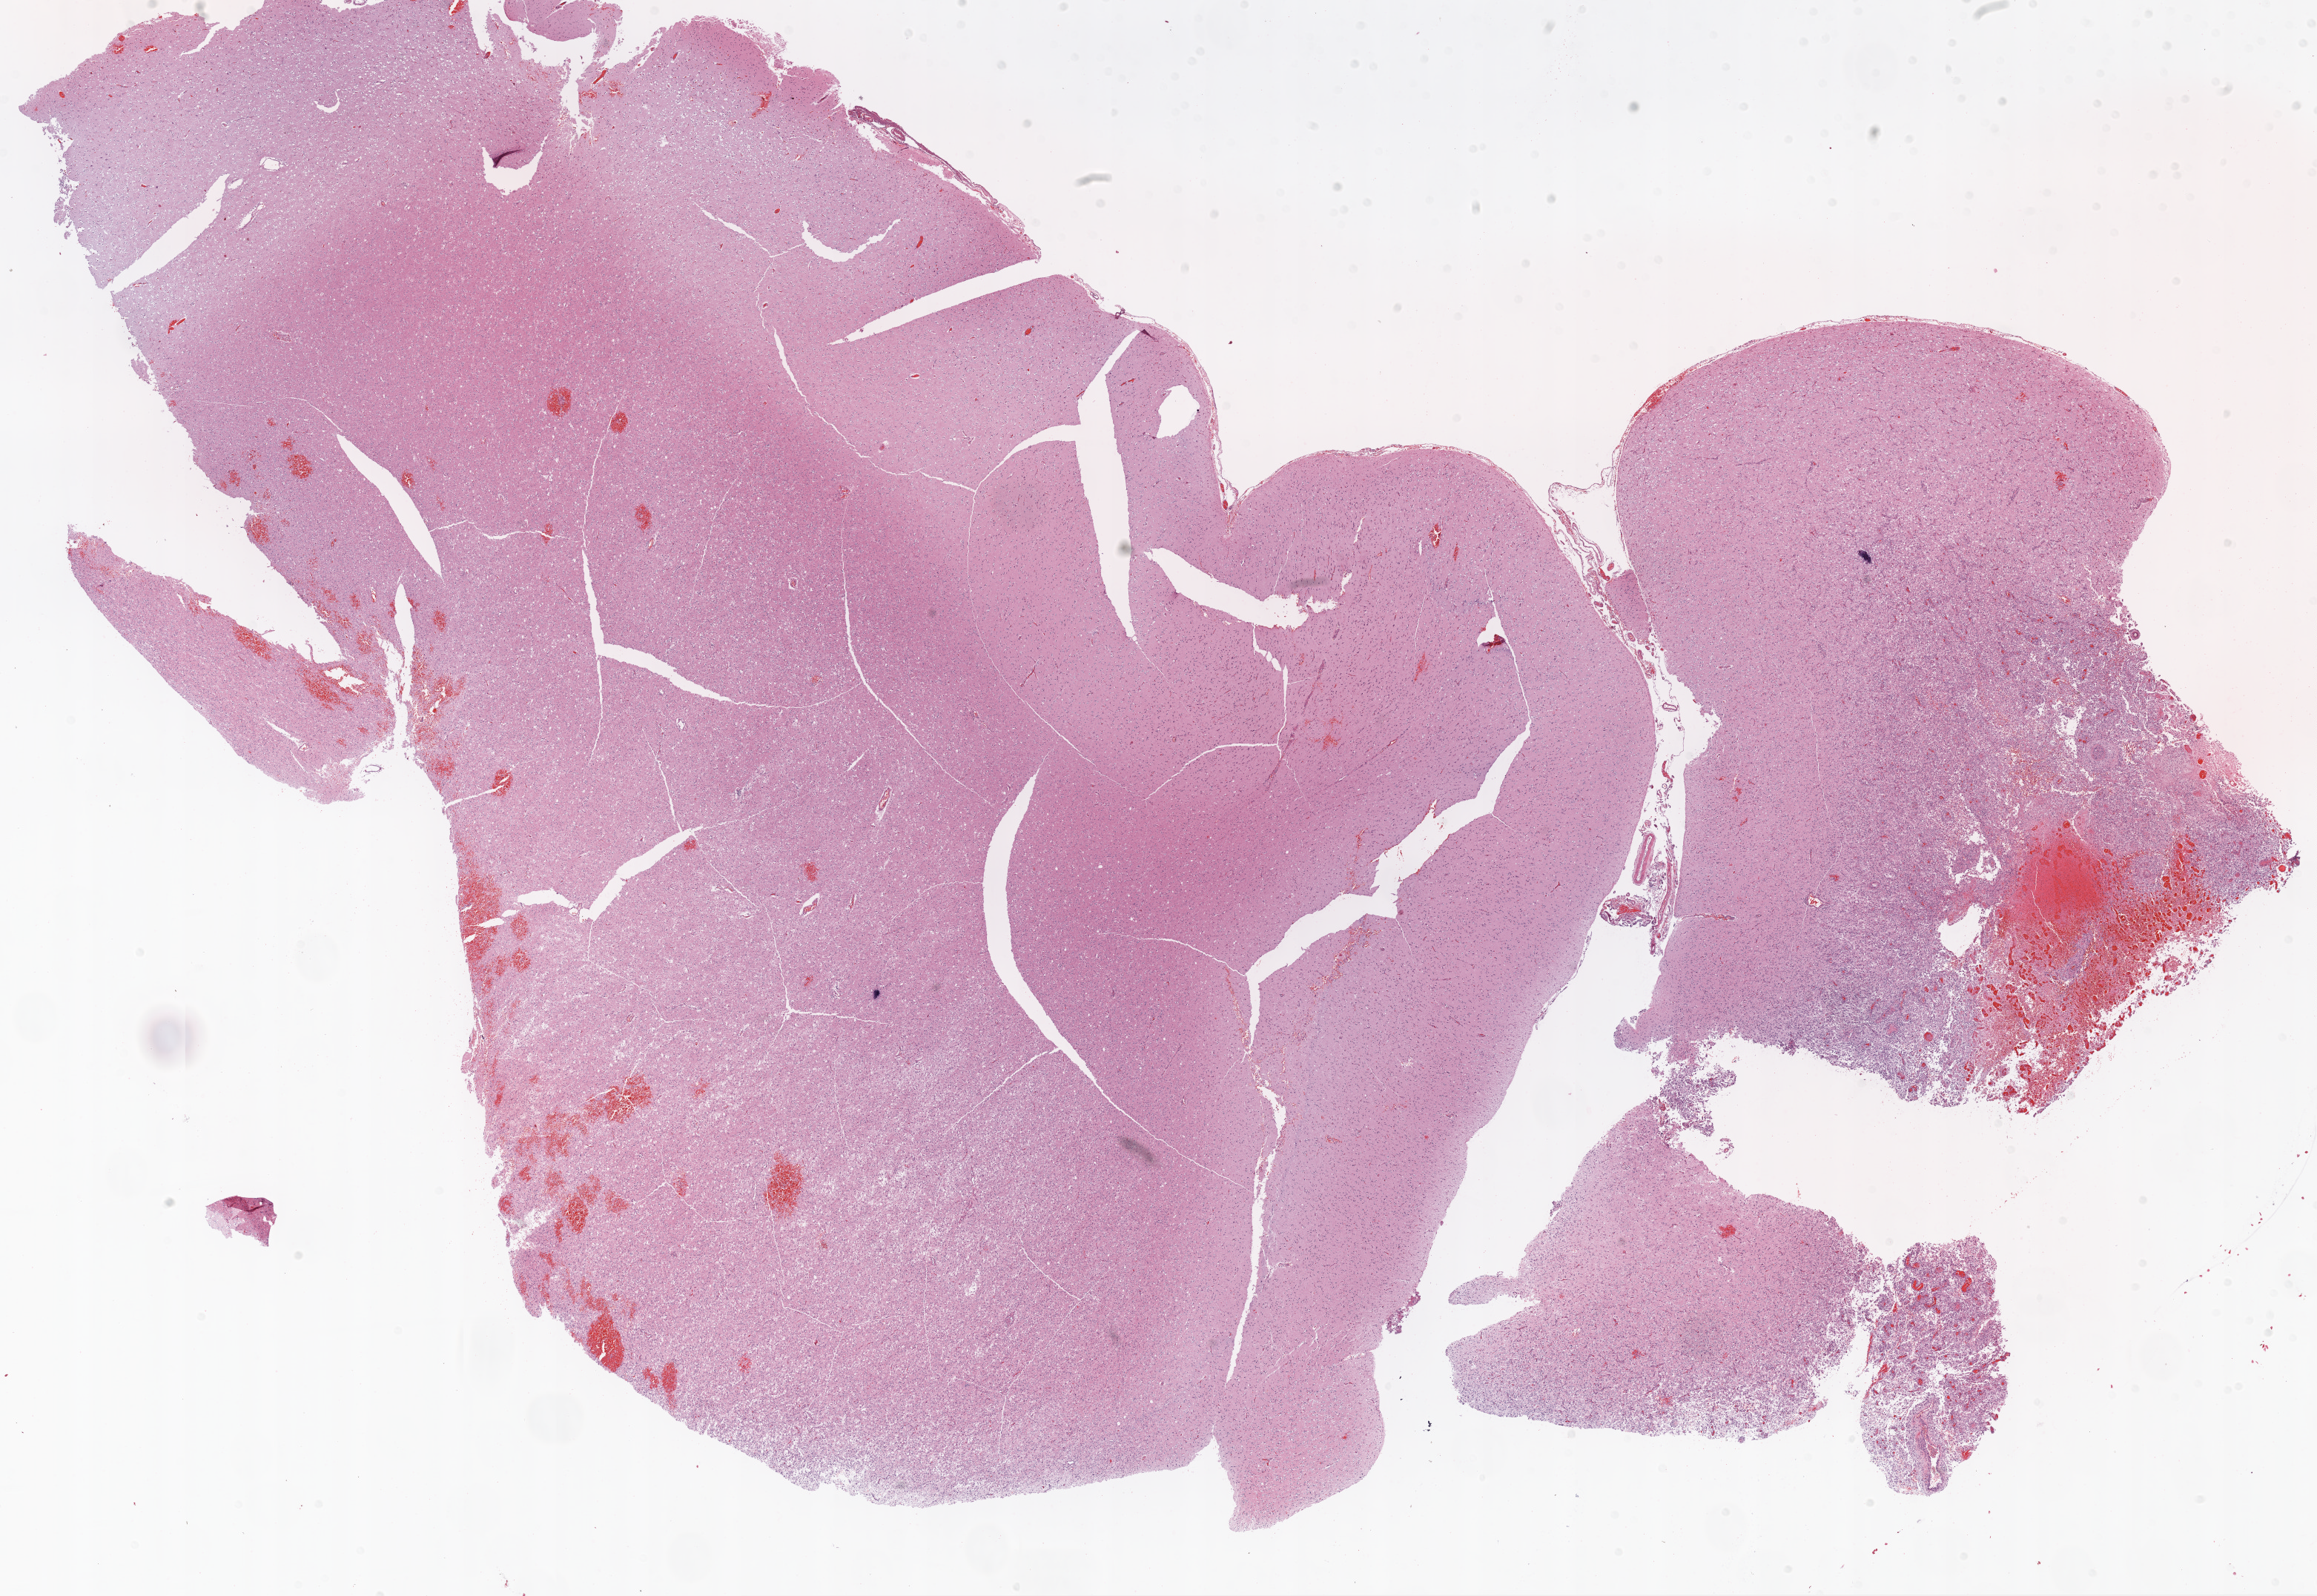
H&E-stained whole-slide image — shown as a low-resolution overview of the whole scanned area (about 25.1 x 17.3 mm, from a 20x scan), FFPE section, sample: primary tumour, brain. Patient: male, age at initial diagnosis 63 years.
Pathologic diagnosis: Glioblastoma.